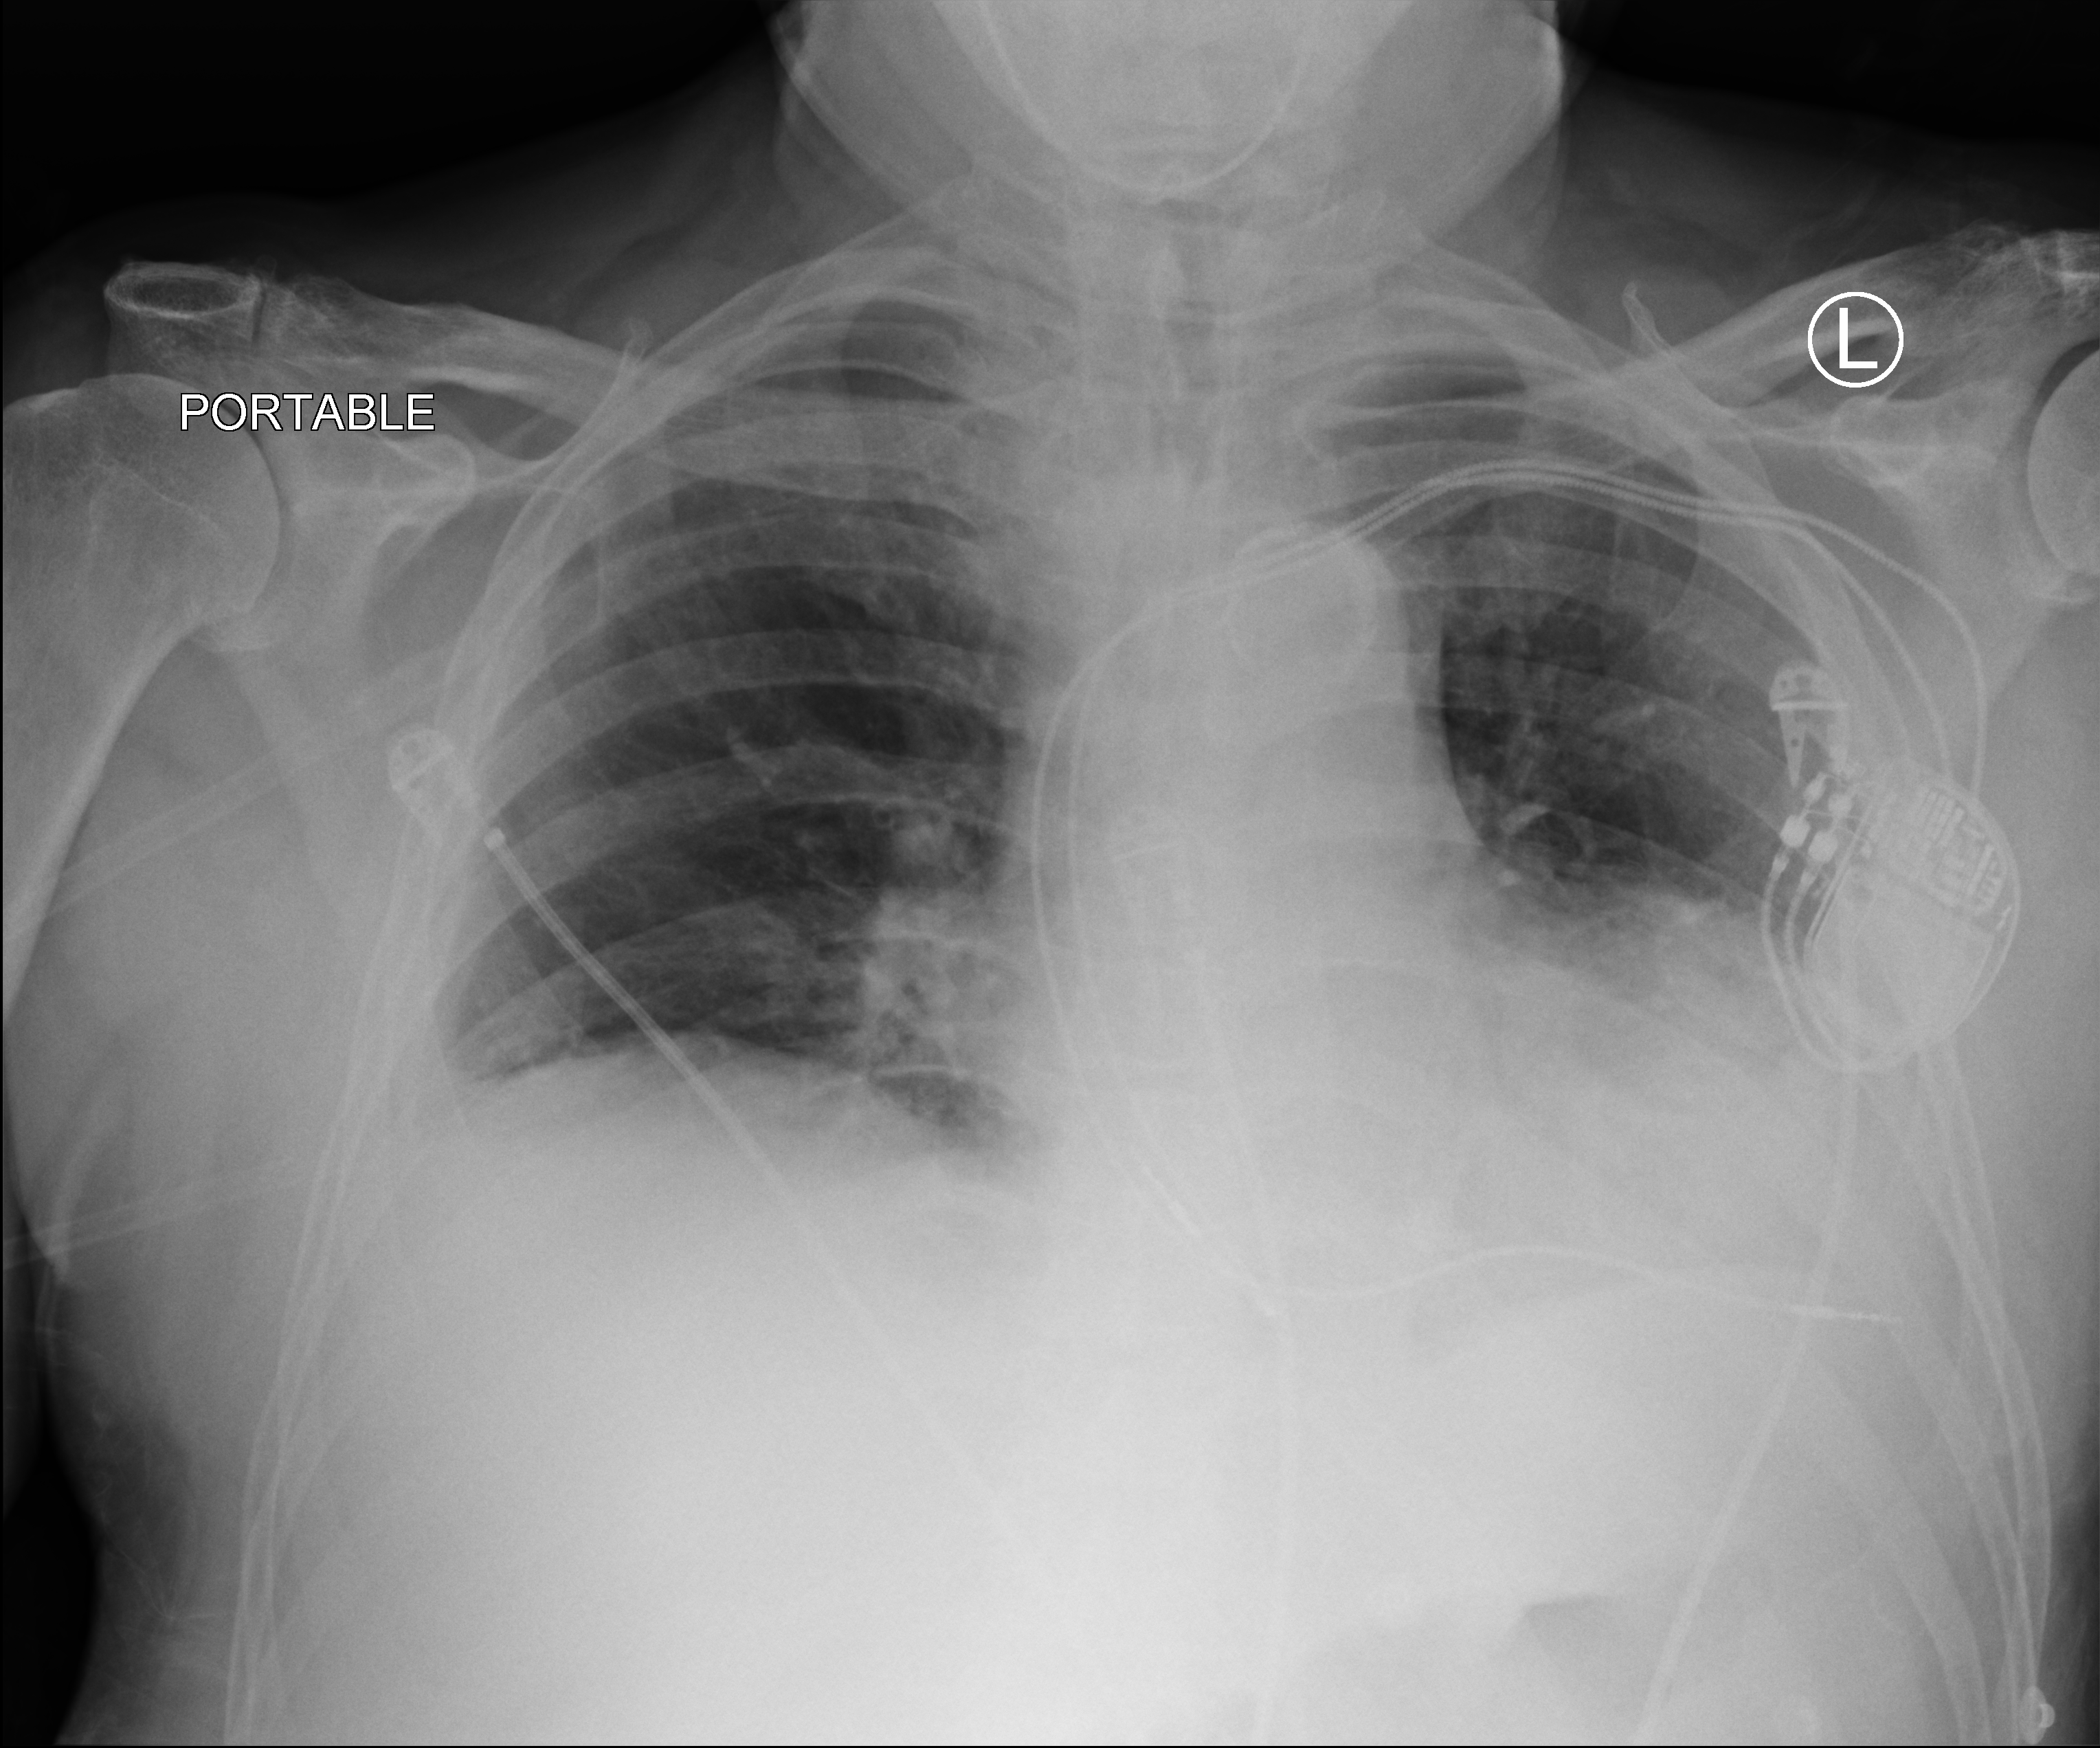
Portable chest radiograph, anteroposterior (AP) projection. Patient hospitalised with COVID-19; male, aged 60–74 years.
Admission-level facts for this patient (not findings on this image; timing relative to this image not recorded): admitted to intensive care during this hospital stay: yes.